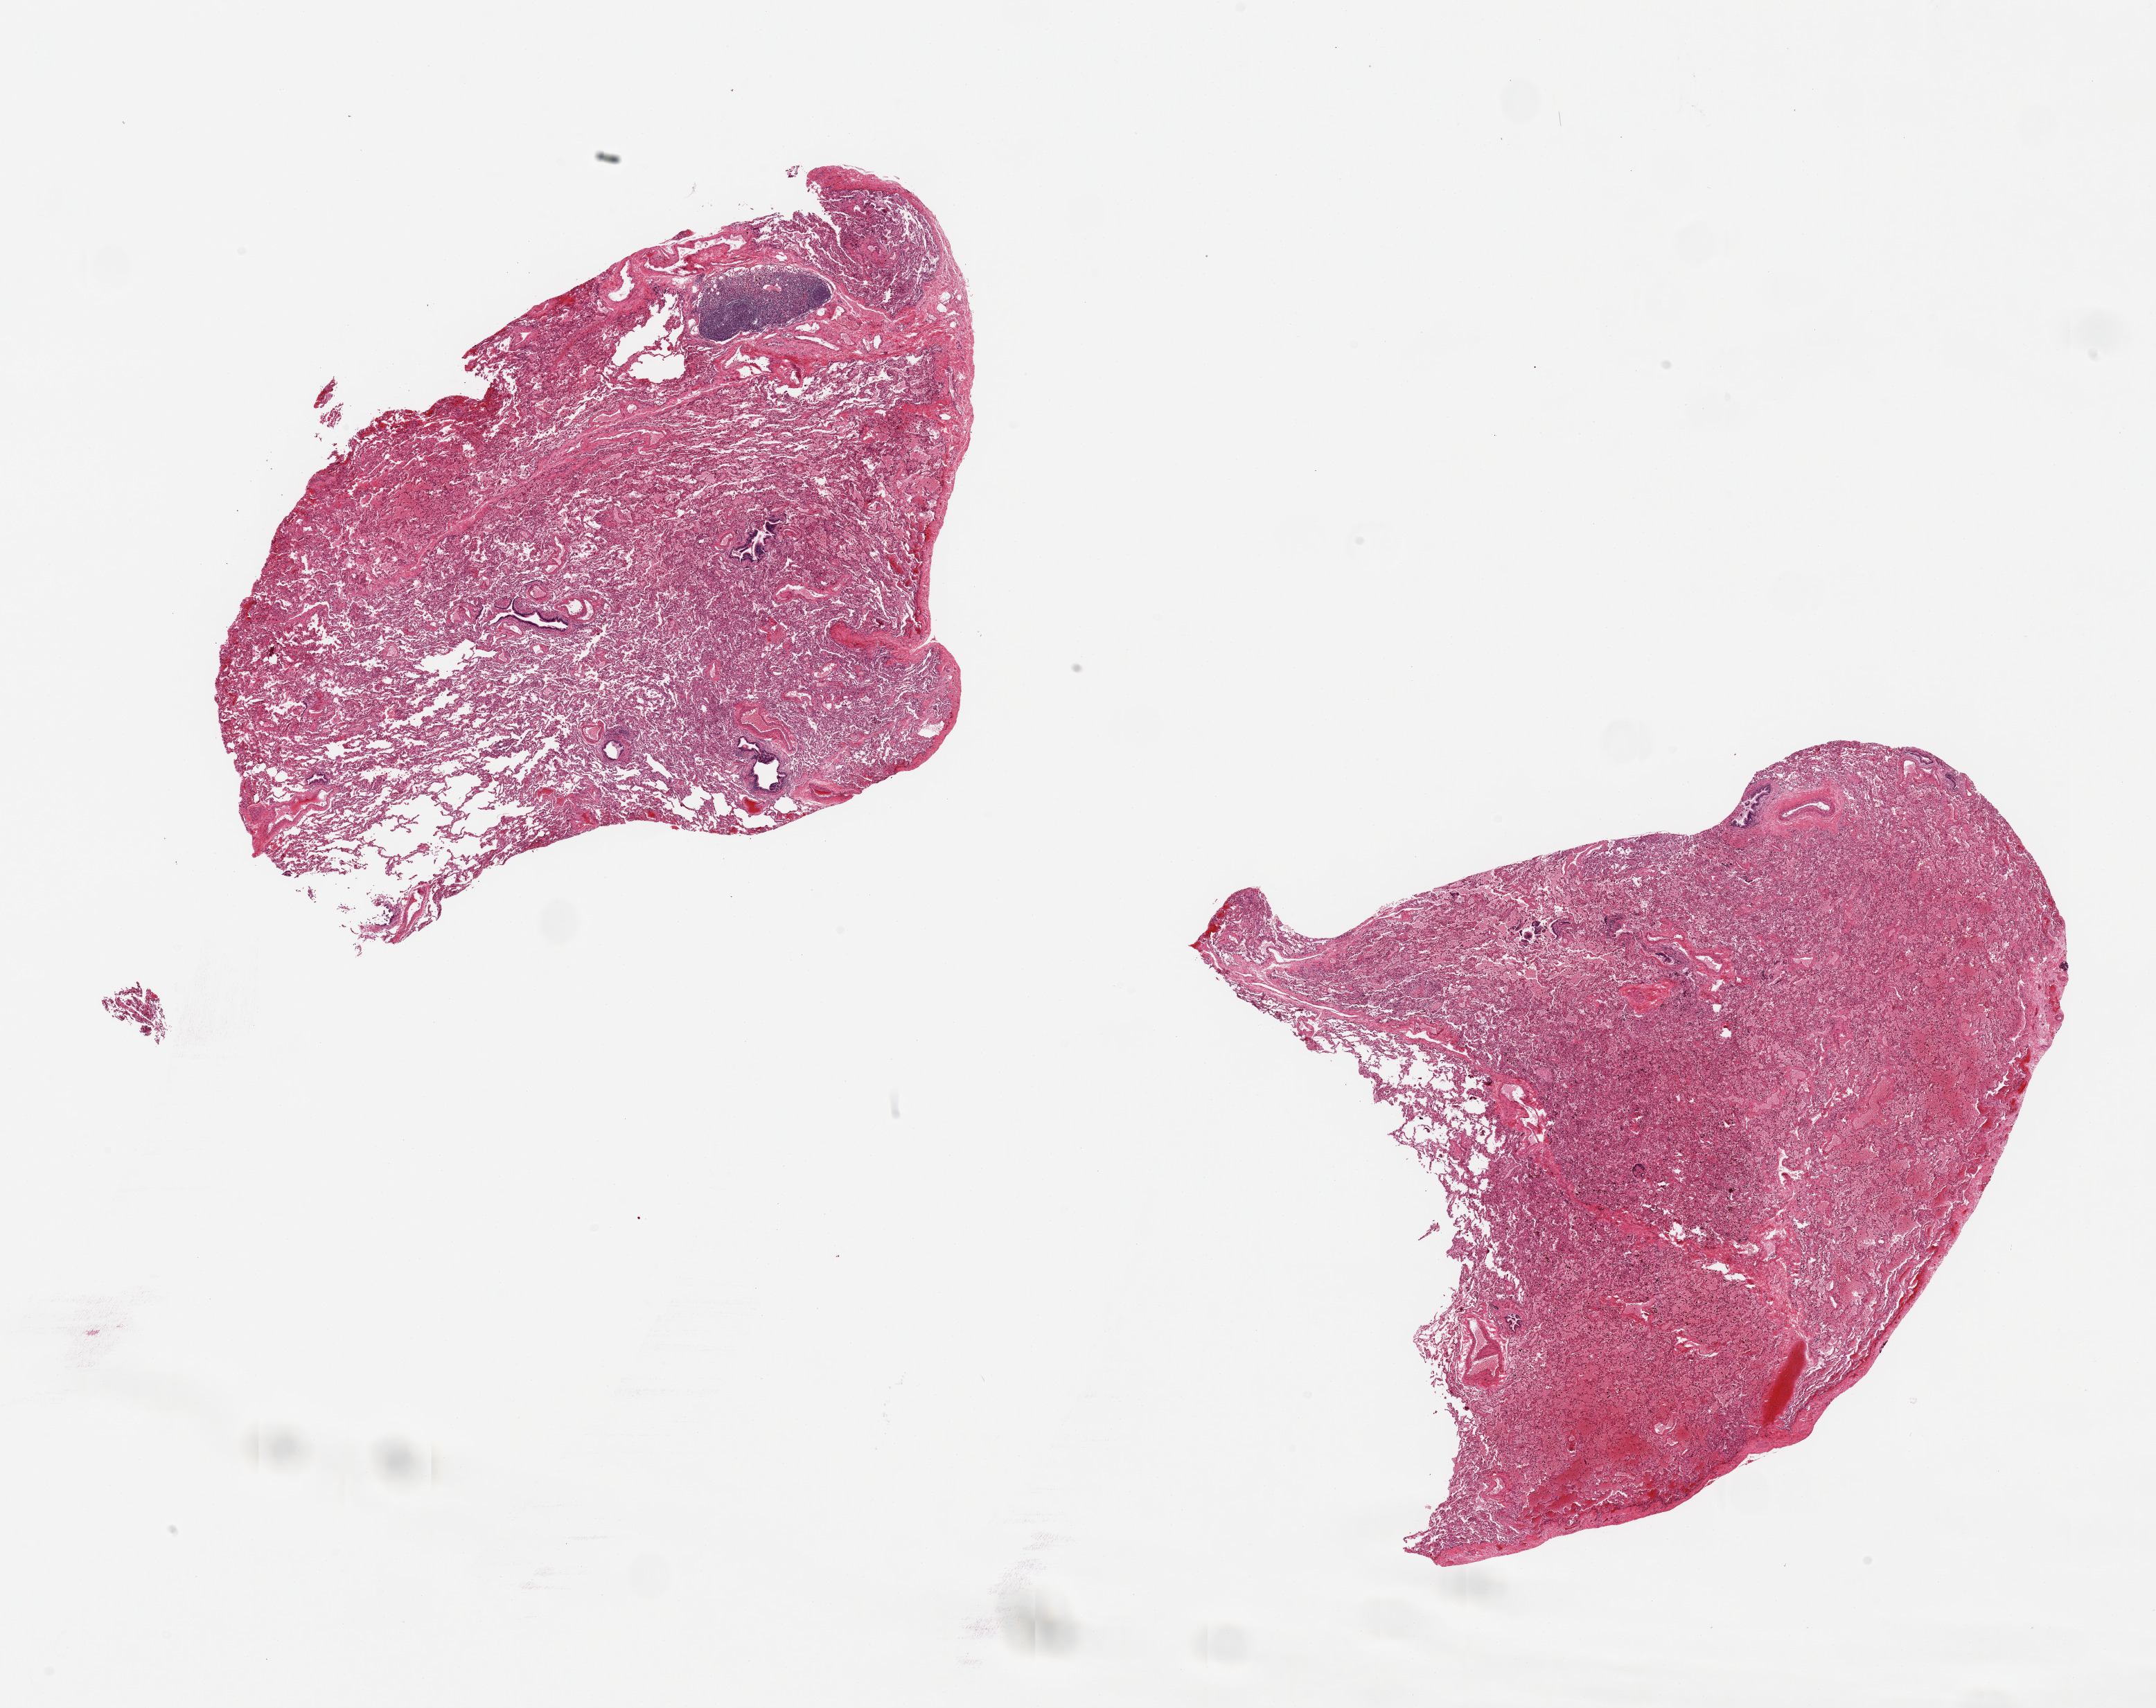
Digitized H&E-stained section, brightfield, a low-resolution overview of the entire scanned area, about 24.6 x 19.5 mm (slide scanned at 20x). PAXgene-fixed paraffin-embedded (PFPE) section. Target tissue: lung. Donor tissue sample. Donor: male.
Pathologist's review note for this sample: 2 pieces ~8x8mm; Atalectatic, focal lymphoid follicle/intrapulmonary lymph node noted.